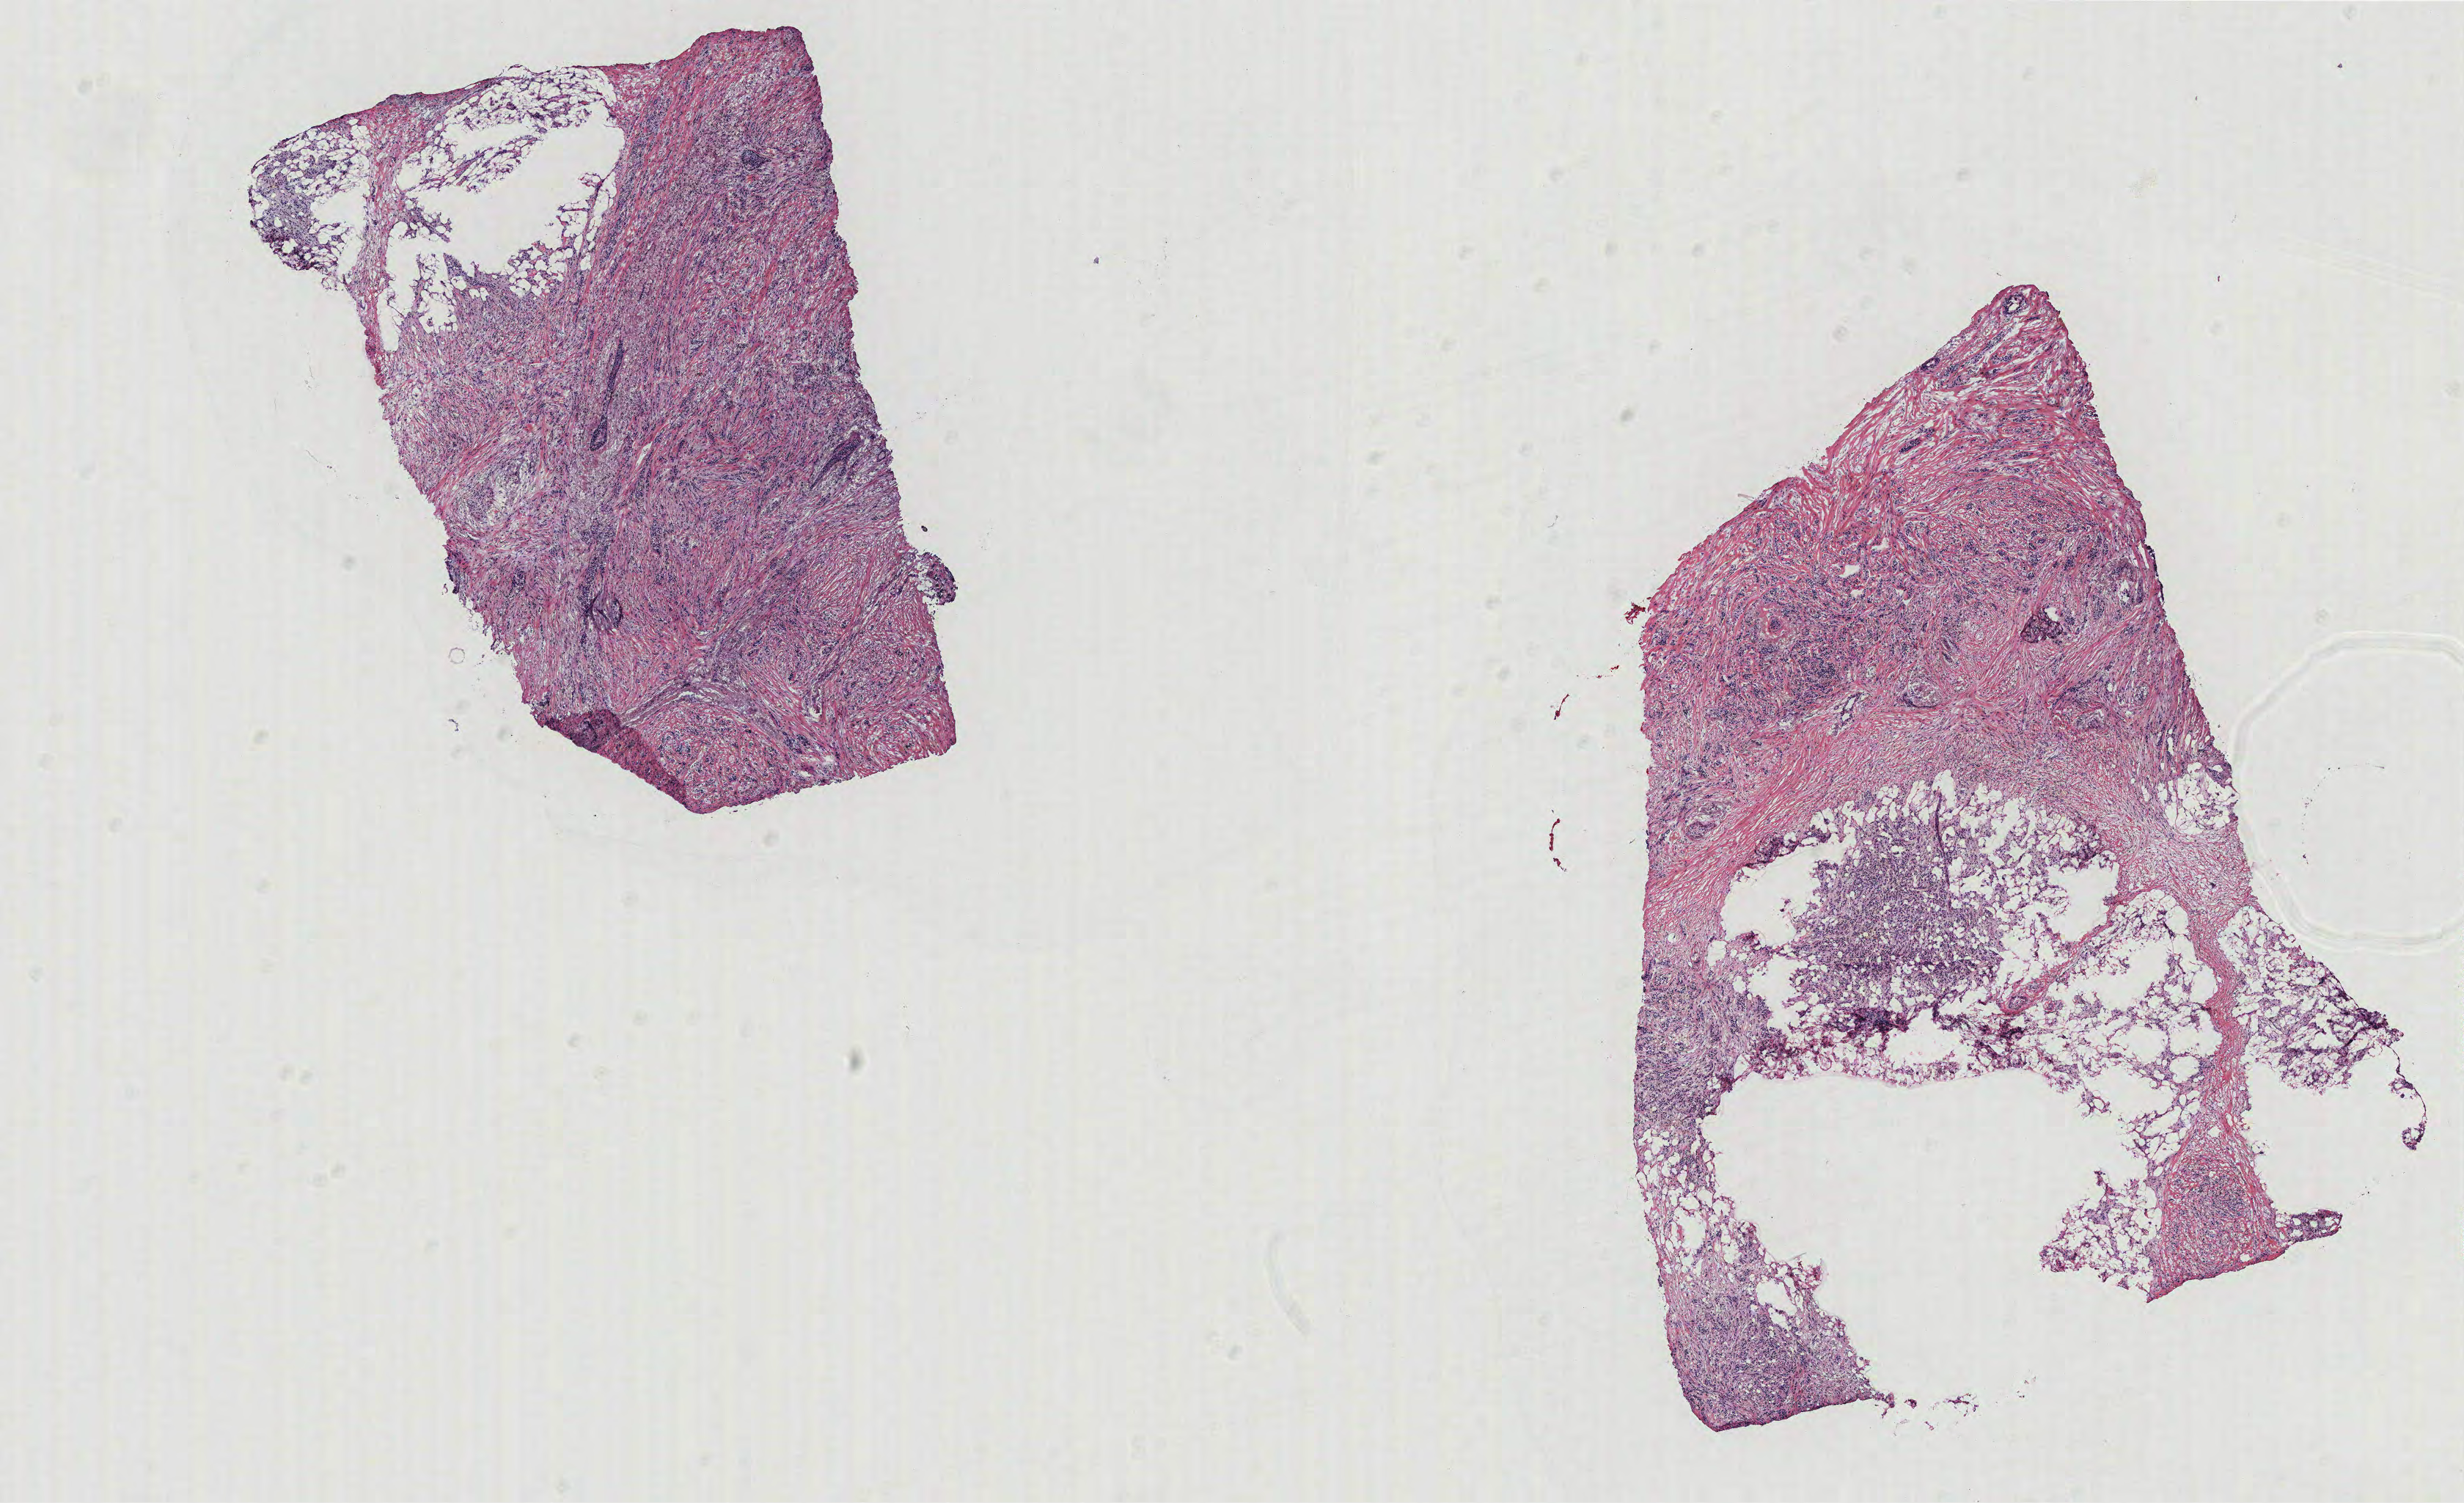
Whole-slide histology image, H&E-stained — whole scanned area (about 13.4 x 8.2 mm) shown as a low-resolution overview. Breast, tissue type not recorded. Patient: female, age 46 years.
• patient diagnosis: Infiltrating duct carcinoma, NOS